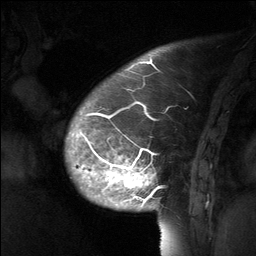
Breast MRI (dynamic contrast-enhanced), one sagittal slice. Slice 15 of 64 in the series (ordered by position). Dynamic contrast-enhanced study with each time point stored as its own series, time point 2 of 3 at this slice position (early post-contrast, ordered by acquisition time). 1.5 T. TE 4.8 ms, TR 27 ms. 2 mm slice thickness. 256 × 256 image matrix, field of view 200 × 200 mm. Female patient, age 39 years. Case-level facts recorded for this patient, not image findings: setting: breast cancer imaged before/during neoadjuvant chemotherapy; receptor status: HER2-positive.
Annotated regions visible in this slice (semi-automatic segmentation, software-assisted and operator-edited):
- analysis volume of interest (the breast-tissue region the enhancement analysis was run in; not a lesion): box from (x=70, y=69) to (x=202, y=224) px
- tumour enhancement mask (voxels above the 90 % enhancement threshold inside the analysis volume of interest): (x=79, y=90)–(x=163, y=204)